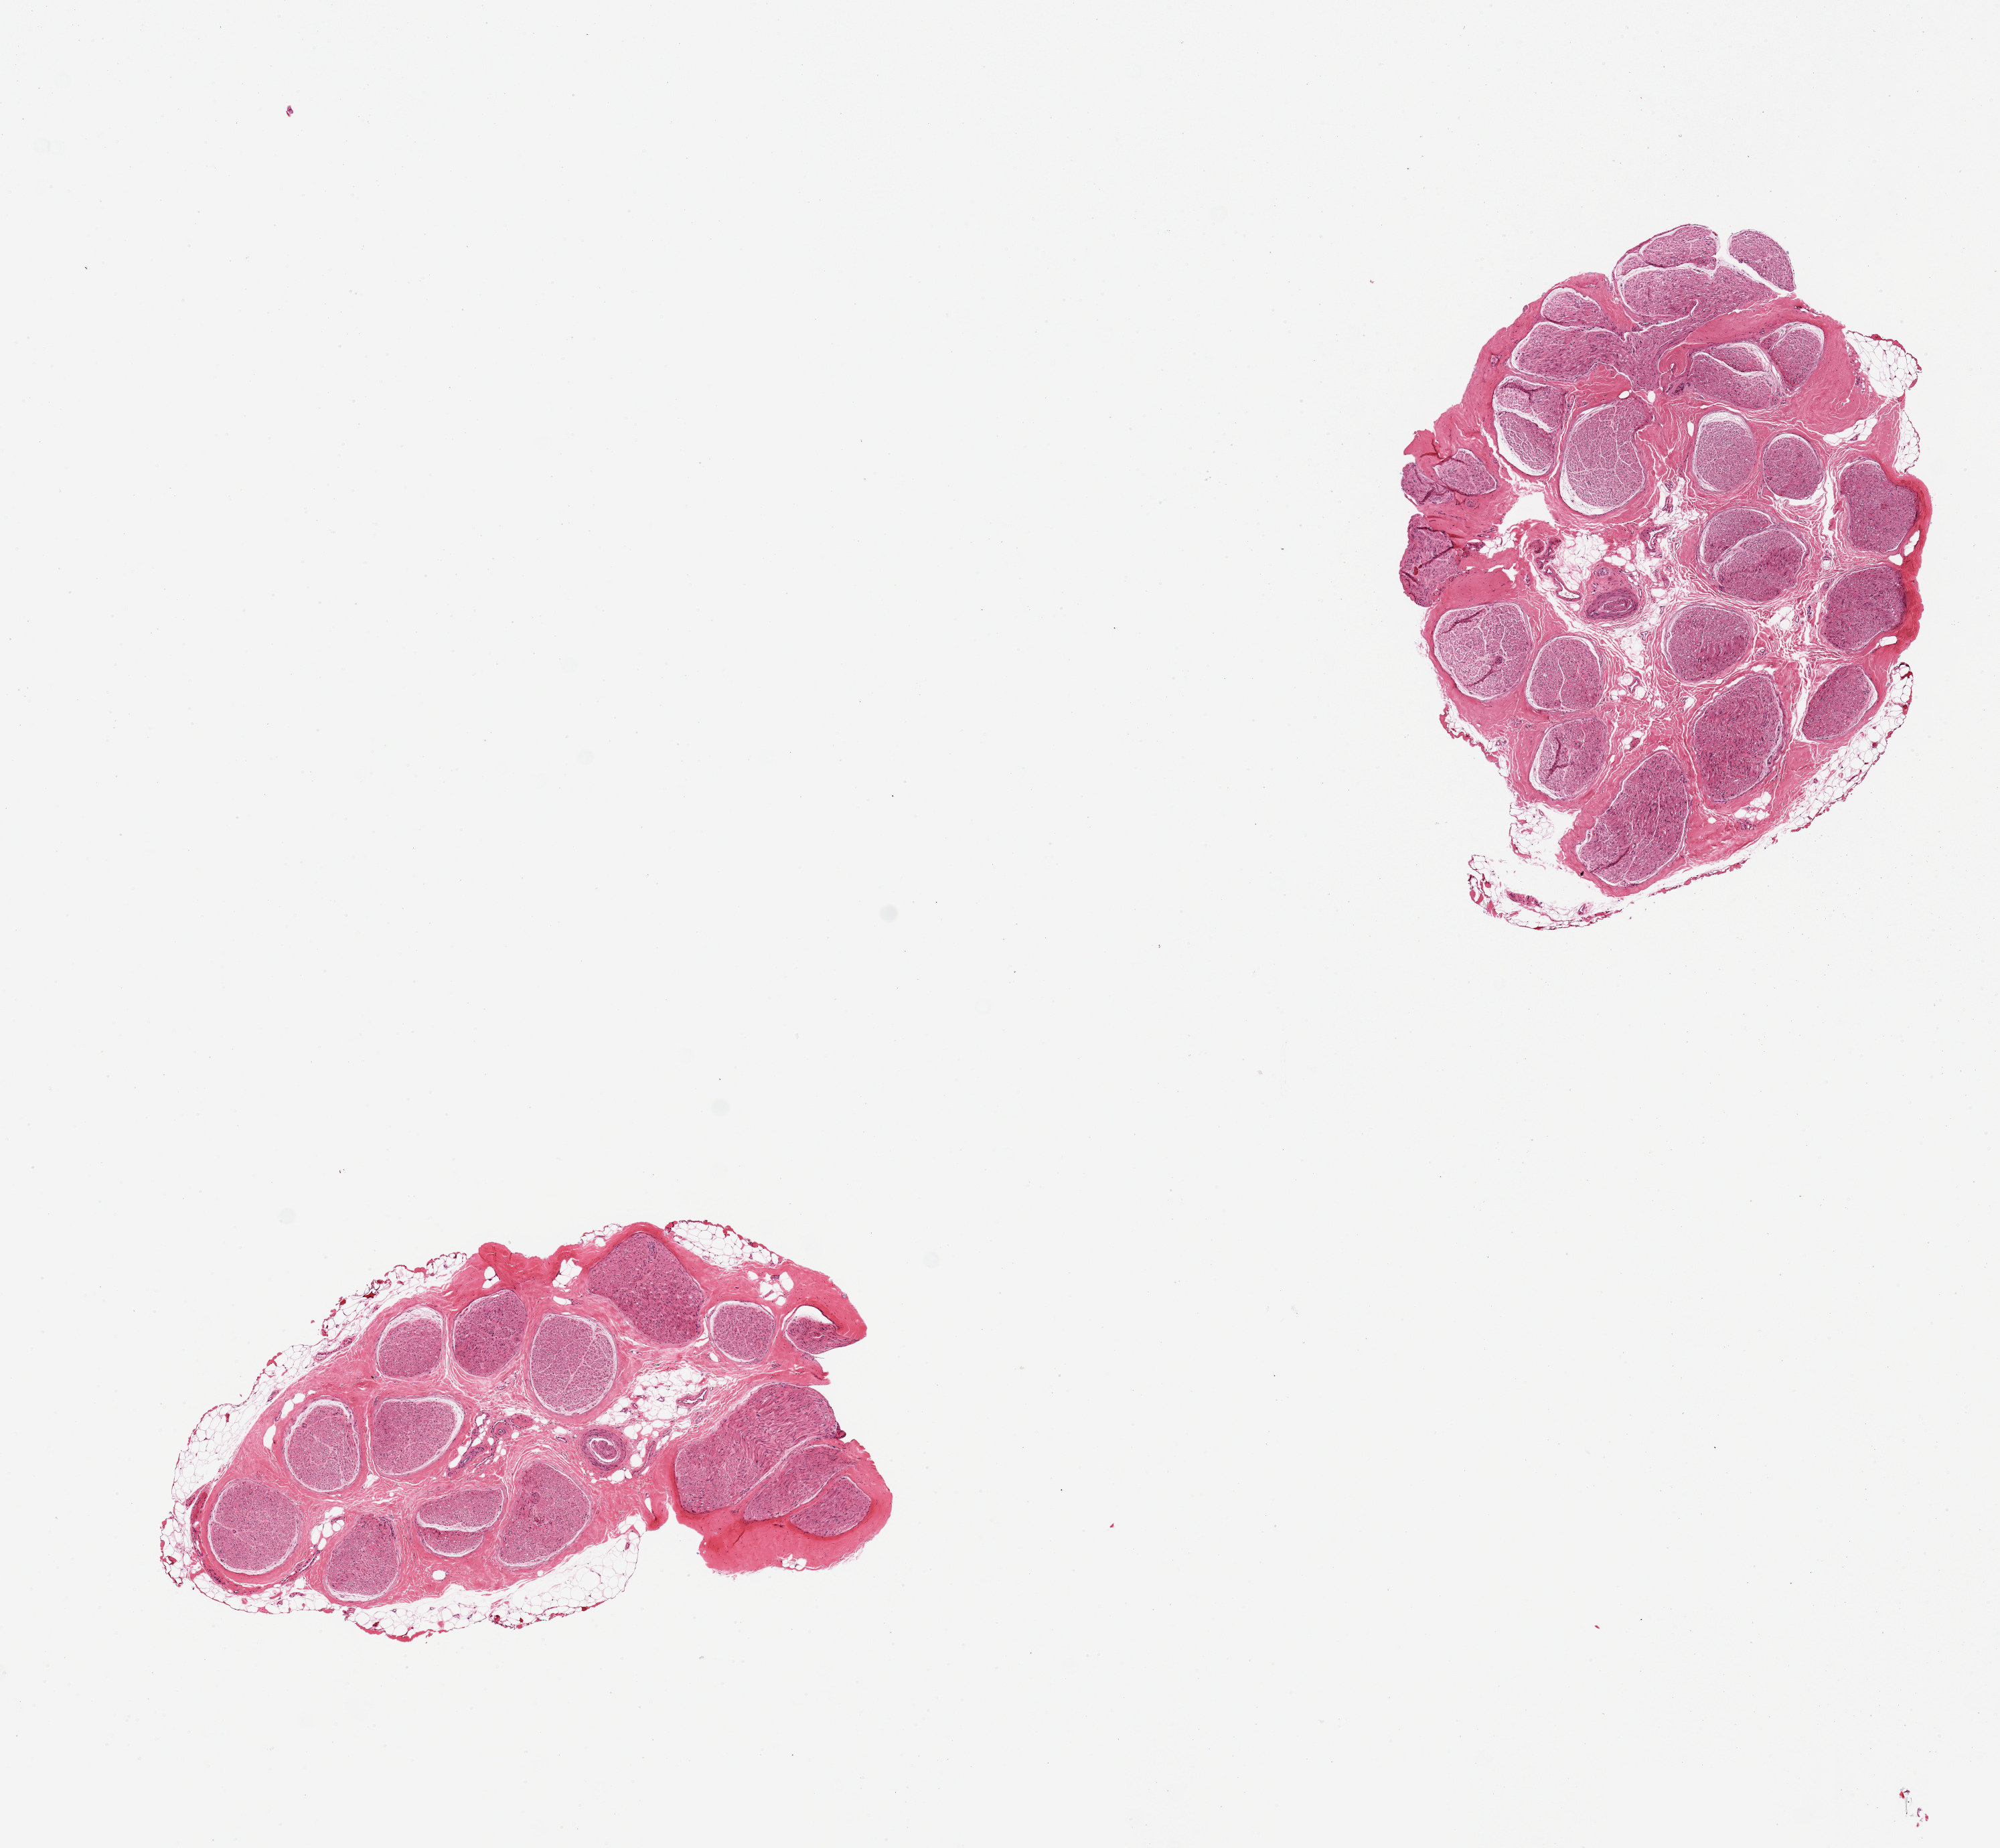
Digitized hematoxylin and eosin (H&E)-stained section, brightfield, a low-resolution overview of the entire scanned area, about 11.8 x 10.9 mm. PAXgene-fixed, paraffin-embedded tissue. Target tissue: tibial nerve. Donor tissue sample. Male donor.
Reviewer comment on this tissue sample: 2 pieces, generally clean specimens.